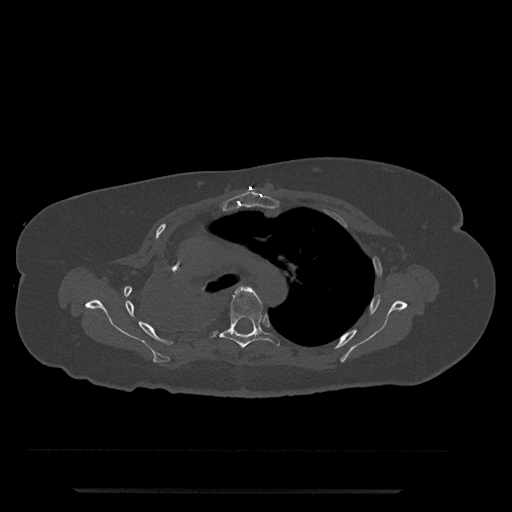
CT including the spine, one axial slice; 120 kVp; bone window (W 1800 / L 400 HU); 0.5 mm slice thickness; 512 × 512 image matrix, field of view 440 × 440 mm. Female patient, age 51 years. From the clinical record (not read from this slice): primary cancer: neuro; vertebrae with lytic lesions (as recorded): T8.
Outlined on this slice (semi-automatically segmented with operator editing):
- T5 vertebra: bounding box (x1, y1, x2, y2) in pixels: (208, 287, 280, 348)